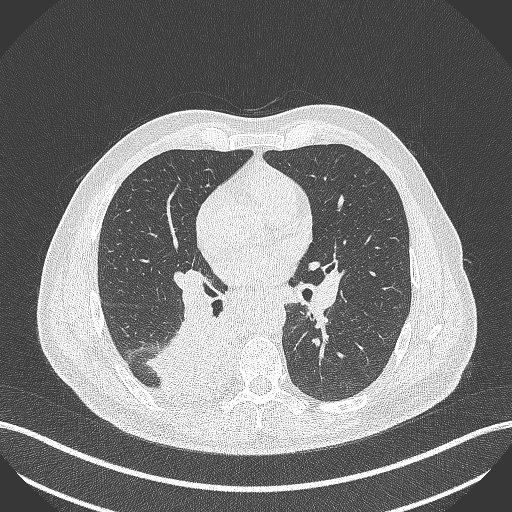
Chest CT, one axial slice; position 250 of 451 along the scan axis; reconstruction kernel B70f; lung window (W 1500 / L -600 HU); 512 × 512 image matrix, field of view 400 × 400 mm. Patient: male, 61 years. Case-level facts recorded for this patient, not image findings: clinical TNM (as recorded): T1 N0 M0; histopathological grade: G3.
Outlined on this slice (rectangle marked by the reading radiologist):
- lung tumour (recorded histology: small cell carcinoma): box from (x=162, y=310) to (x=241, y=400) px